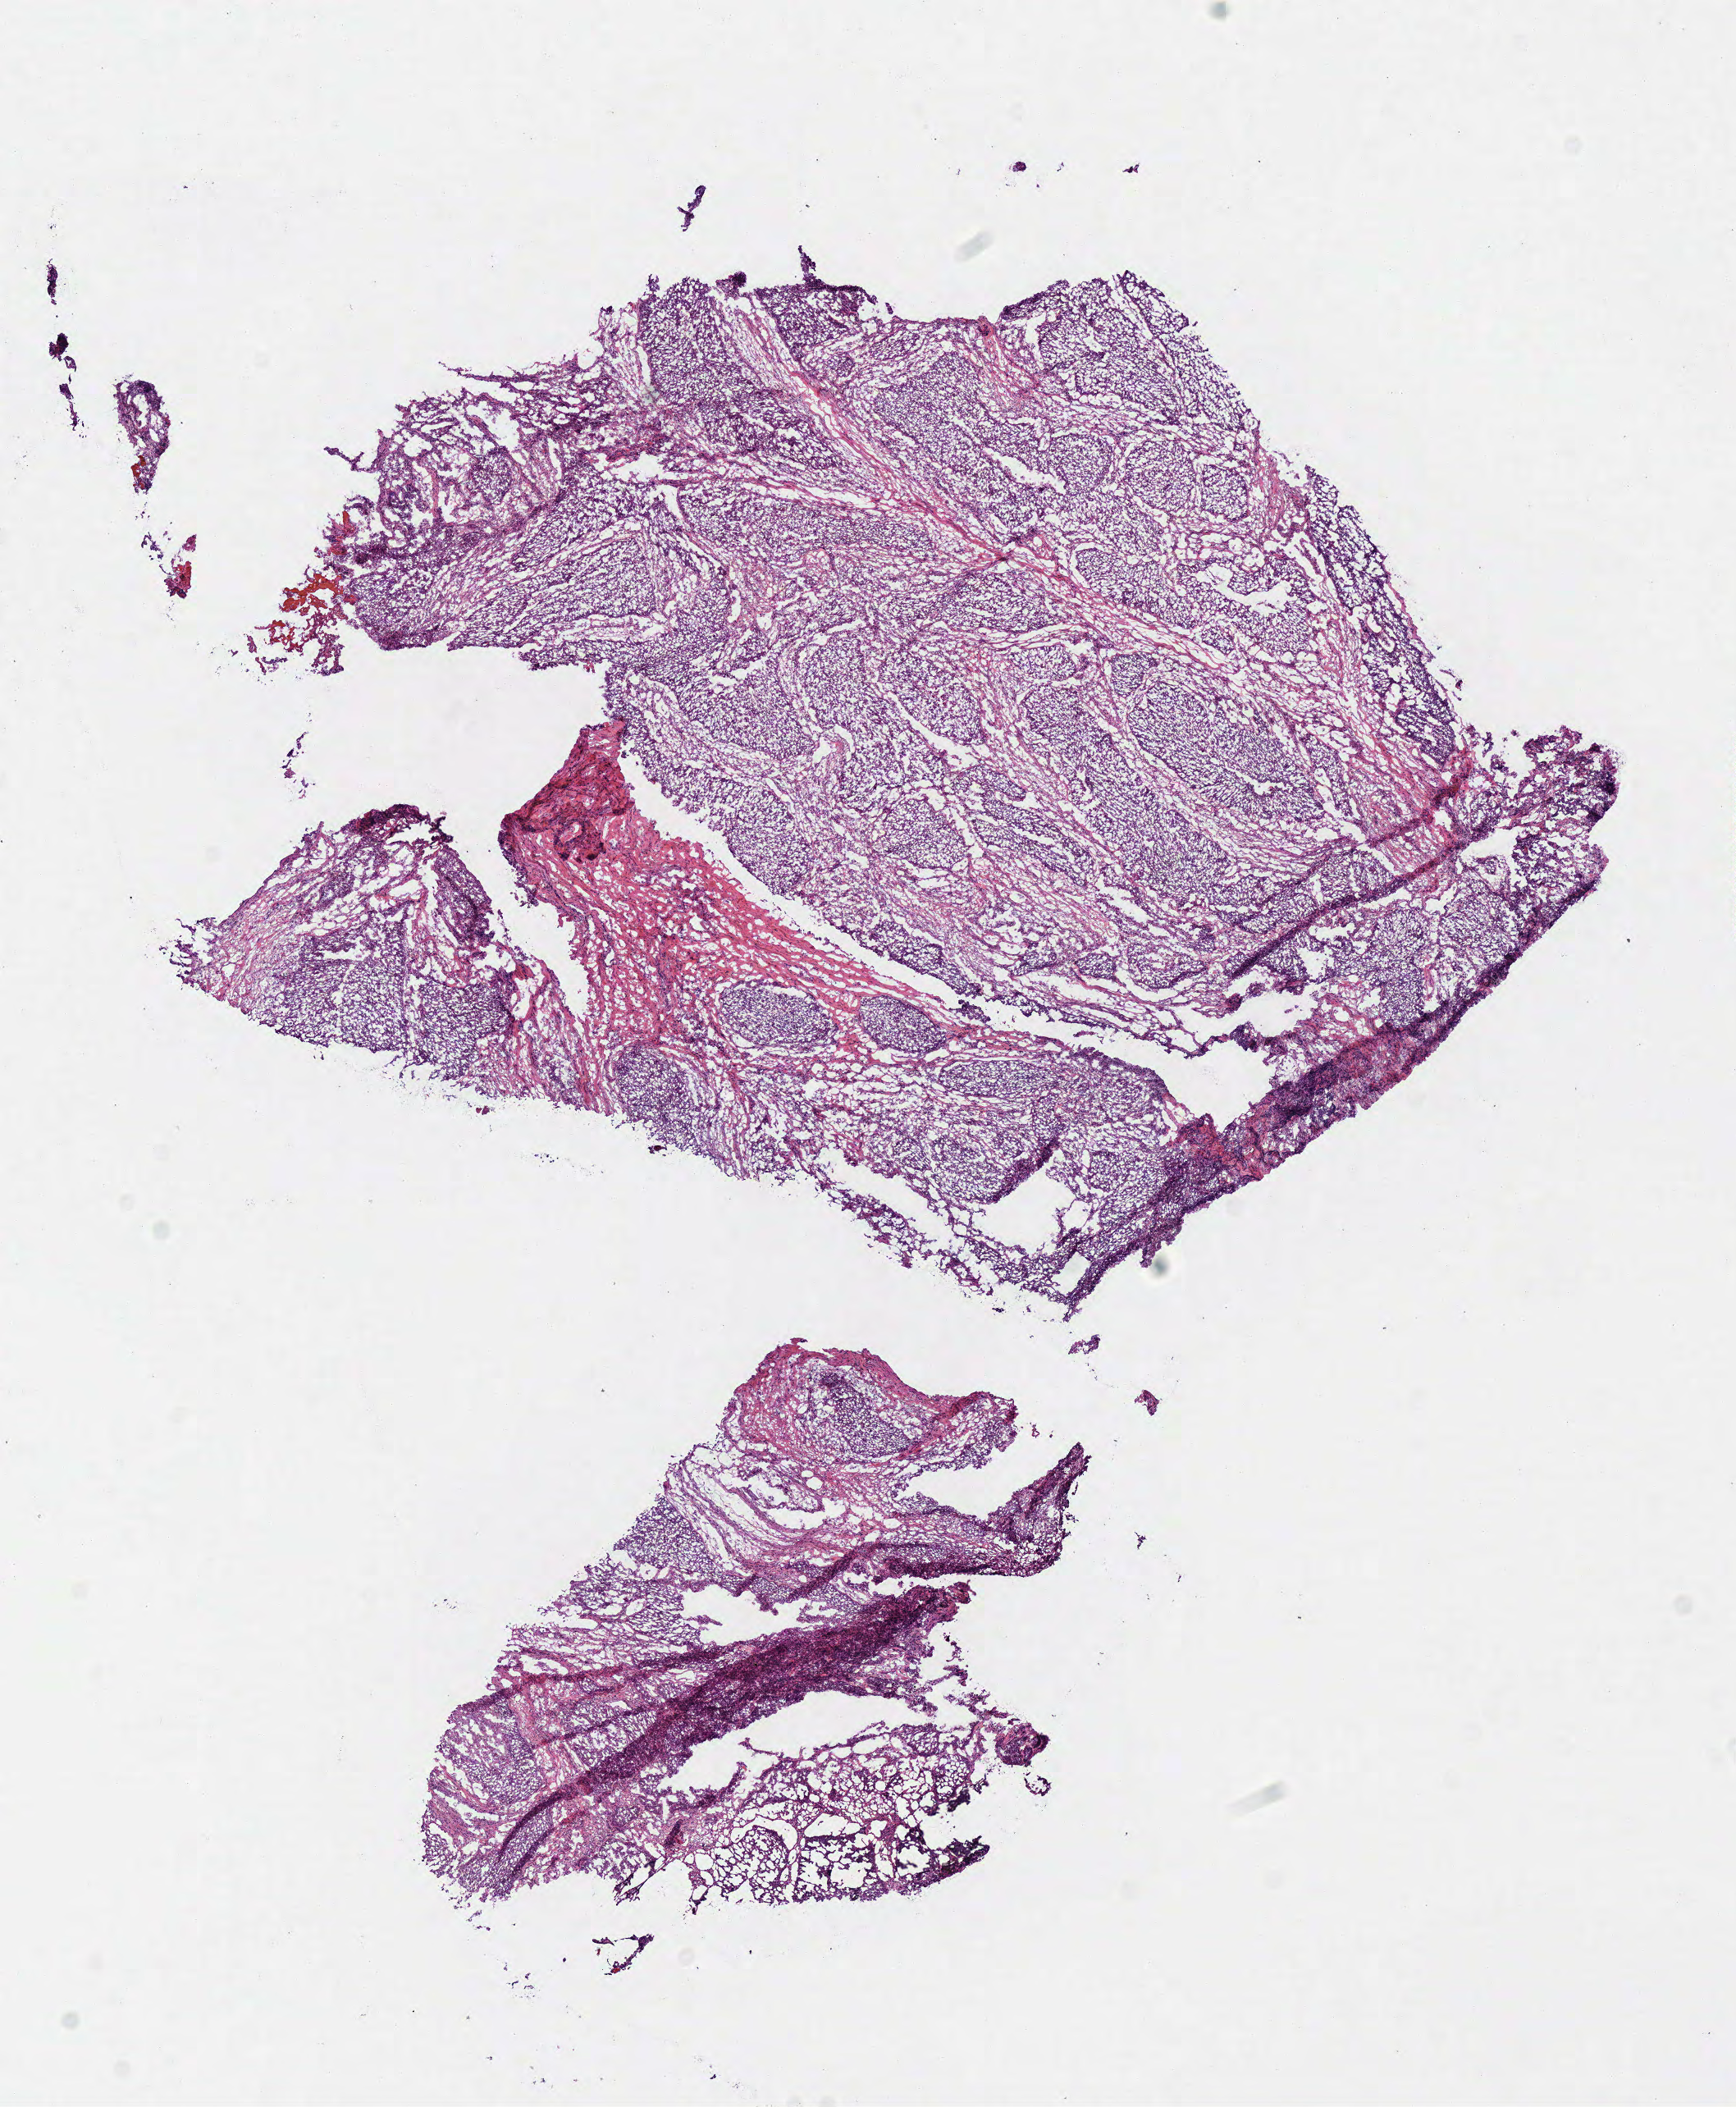
Digitized Hematoxylin and eosin (H&E) stained tissue section (whole slide), shown as a low-resolution overview of the whole scanned area (about 8.3 x 10.1 mm), frozen section from the top of the tissue portion, primary tumour sample from the head and neck. Male patient; age at initial diagnosis 66 years. Histologic grade: G3 (poorly differentiated). Composition of this section per pathologist review: tumour cells 85%, tumour nuclei 75%, normal cells 0%, stromal cells 15%, necrosis 0%.
Diagnosis: Squamous cell carcinoma, NOS (overlapping lesion of lip, oral cavity and pharynx). AJCC pathologic stage: III (7th edition).